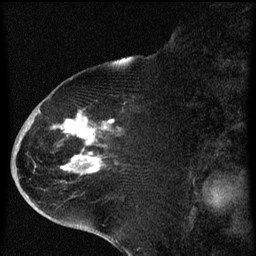
Breast MRI (dynamic contrast-enhanced), one sagittal slice; position 28 of 60 along the scan axis; dynamic contrast-enhanced series, image 2 of 4 at this slice position (ordered by acquisition); 1.5 T; TE 4.2 ms, TR 8 ms; 2 mm slice thickness; 256 × 256 image matrix. Female patient, age 71 years.
Annotated regions visible in this slice (semi-automatically segmented with operator editing):
- analysis volume of interest (the breast-tissue region the enhancement analysis was run in; not a lesion): bounding box (x1, y1, x2, y2) in pixels: (32, 86, 125, 205)
- tumour enhancement mask (voxels above the 70 % enhancement threshold inside the analysis volume of interest): (38, 110, 121, 173)